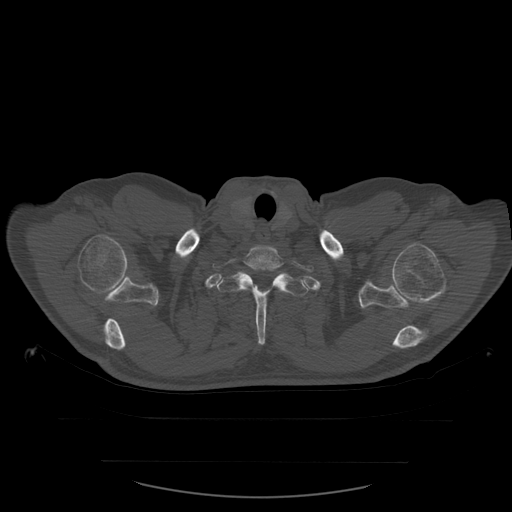
CT including the spine, one axial slice. Position 481 of 590 along the scan axis. Bone window (W 1800 / L 400 HU). 512 × 512 image matrix, field of view 479 × 479 mm. Patient age 71 years. Case-level facts recorded for this patient, not image findings: primary cancer: lung; vertebrae with lytic lesions (as recorded): T1, T2, L5, S1.
Structures marked on this image (semi-automatic segmentation, software-assisted and operator-edited):
- T1 vertebra: bounding box (x1, y1, x2, y2) in pixels: (213, 246, 314, 289)
- T2 vertebra: (217, 272, 311, 345)